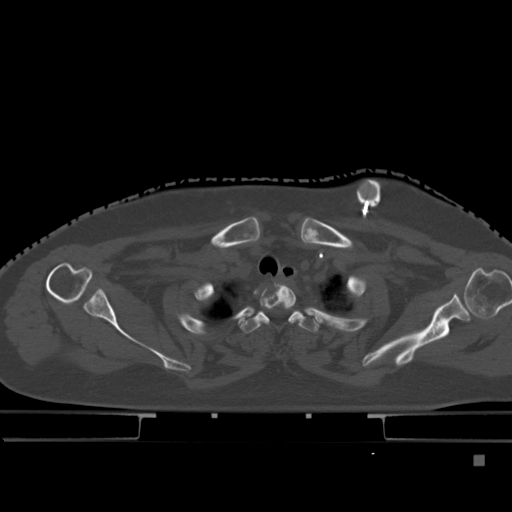
CT including the spine, one axial slice; slice 364 of 495 in the series (ordered by position); bone window (W 1800 / L 400 HU); 1.5 mm slice thickness; 512 × 512 image matrix. Female patient, age 33 years. Case-level facts recorded for this patient, not image findings: primary cancer: breast; vertebrae with lytic lesions (as recorded): T1.
Structures marked on this image (semi-automatically segmented with operator editing):
- T1 vertebra: bounding box <260,283,296,327> (left, top, right, bottom; pixels)
- T2 vertebra: <238,310,342,333>